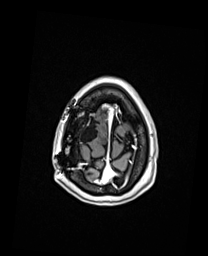
Brain MRI from a brain-tumour surgery series, one axial slice. Slice 29 of 192 in the series (ordered by position). T1-weighted post-contrast. 1 mm slice thickness. 208 × 256 image matrix, field of view 208 × 256 mm. Case-level facts recorded for this patient, not image findings: histopathology: Oligodendroglioma; WHO grade: 3; IDH mutation: yes; tumour location: Right Frontal.
Outlined on this slice (expert manual segmentation):
- previous resection cavity: bounding box (x1, y1, x2, y2) in pixels: (72, 118, 99, 142)